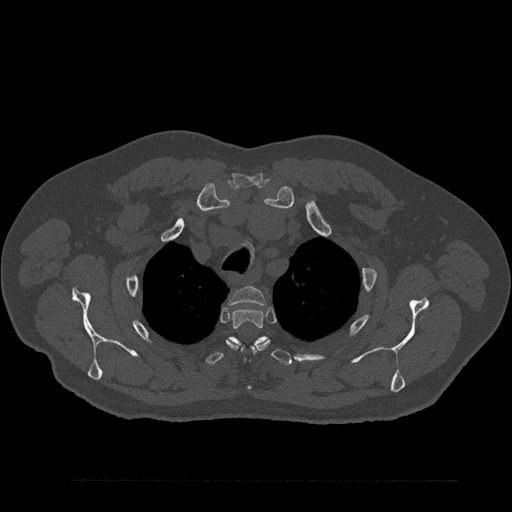
CT including the spine, one axial slice. Slice 678 of 797 in the series (ordered by position). Reconstruction kernel Br40s/3. Bone window (W 1800 / L 400 HU). 0.5 mm slice thickness. 512 × 512 image matrix, field of view 430 × 430 mm. Patient: male, 61 years. Case-level facts recorded for this patient, not image findings: primary cancer: prostate.
Outlined on this slice (semi-automatic segmentation, software-assisted and operator-edited):
- T2 vertebra: box from (x=230, y=287) to (x=266, y=306) px
- T3 vertebra: (x=226, y=308)–(x=270, y=389)
- T4 vertebra: (x=205, y=336)–(x=292, y=366)